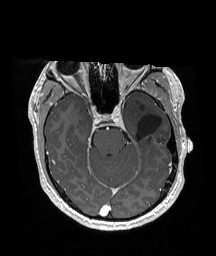
Brain MRI from a brain-tumour surgery series, one axial slice. Position 117 of 192 along the scan axis. T1-weighted post-contrast. 216 × 256 image matrix, field of view 211 × 250 mm. Case-level facts recorded for this patient, not image findings: histopathology: Glioneuronal tumor; WHO grade: 2.
Outlined on this slice (manually delineated by an expert):
- previous resection cavity: bounding box (x1, y1, x2, y2) in pixels: (137, 113, 161, 139)